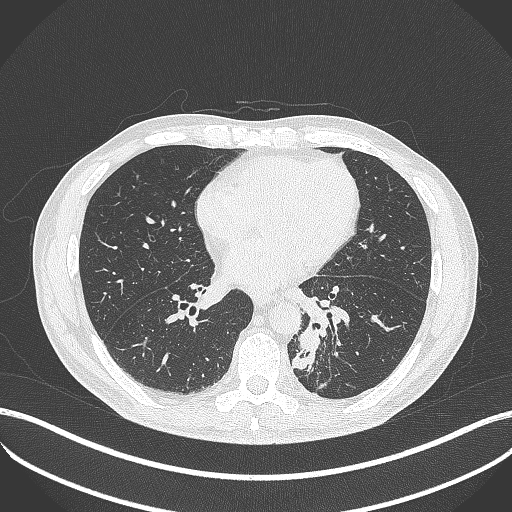
Chest CT, one axial slice; reconstruction kernel B70f; 120 kVp; lung window (W 1500 / L -600 HU); 1 mm slice thickness; 512 × 512 image matrix, field of view 400 × 400 mm. Male patient, age 72 years. Case-level facts recorded for this patient, not image findings: clinical TNM (as recorded): T2b N0 M1.
Annotated regions visible in this slice (rectangle marked by the reading radiologist):
- lung tumour (recorded histology: adenocarcinoma): bounding box [x1, y1, x2, y2] px = [294, 318, 325, 375]